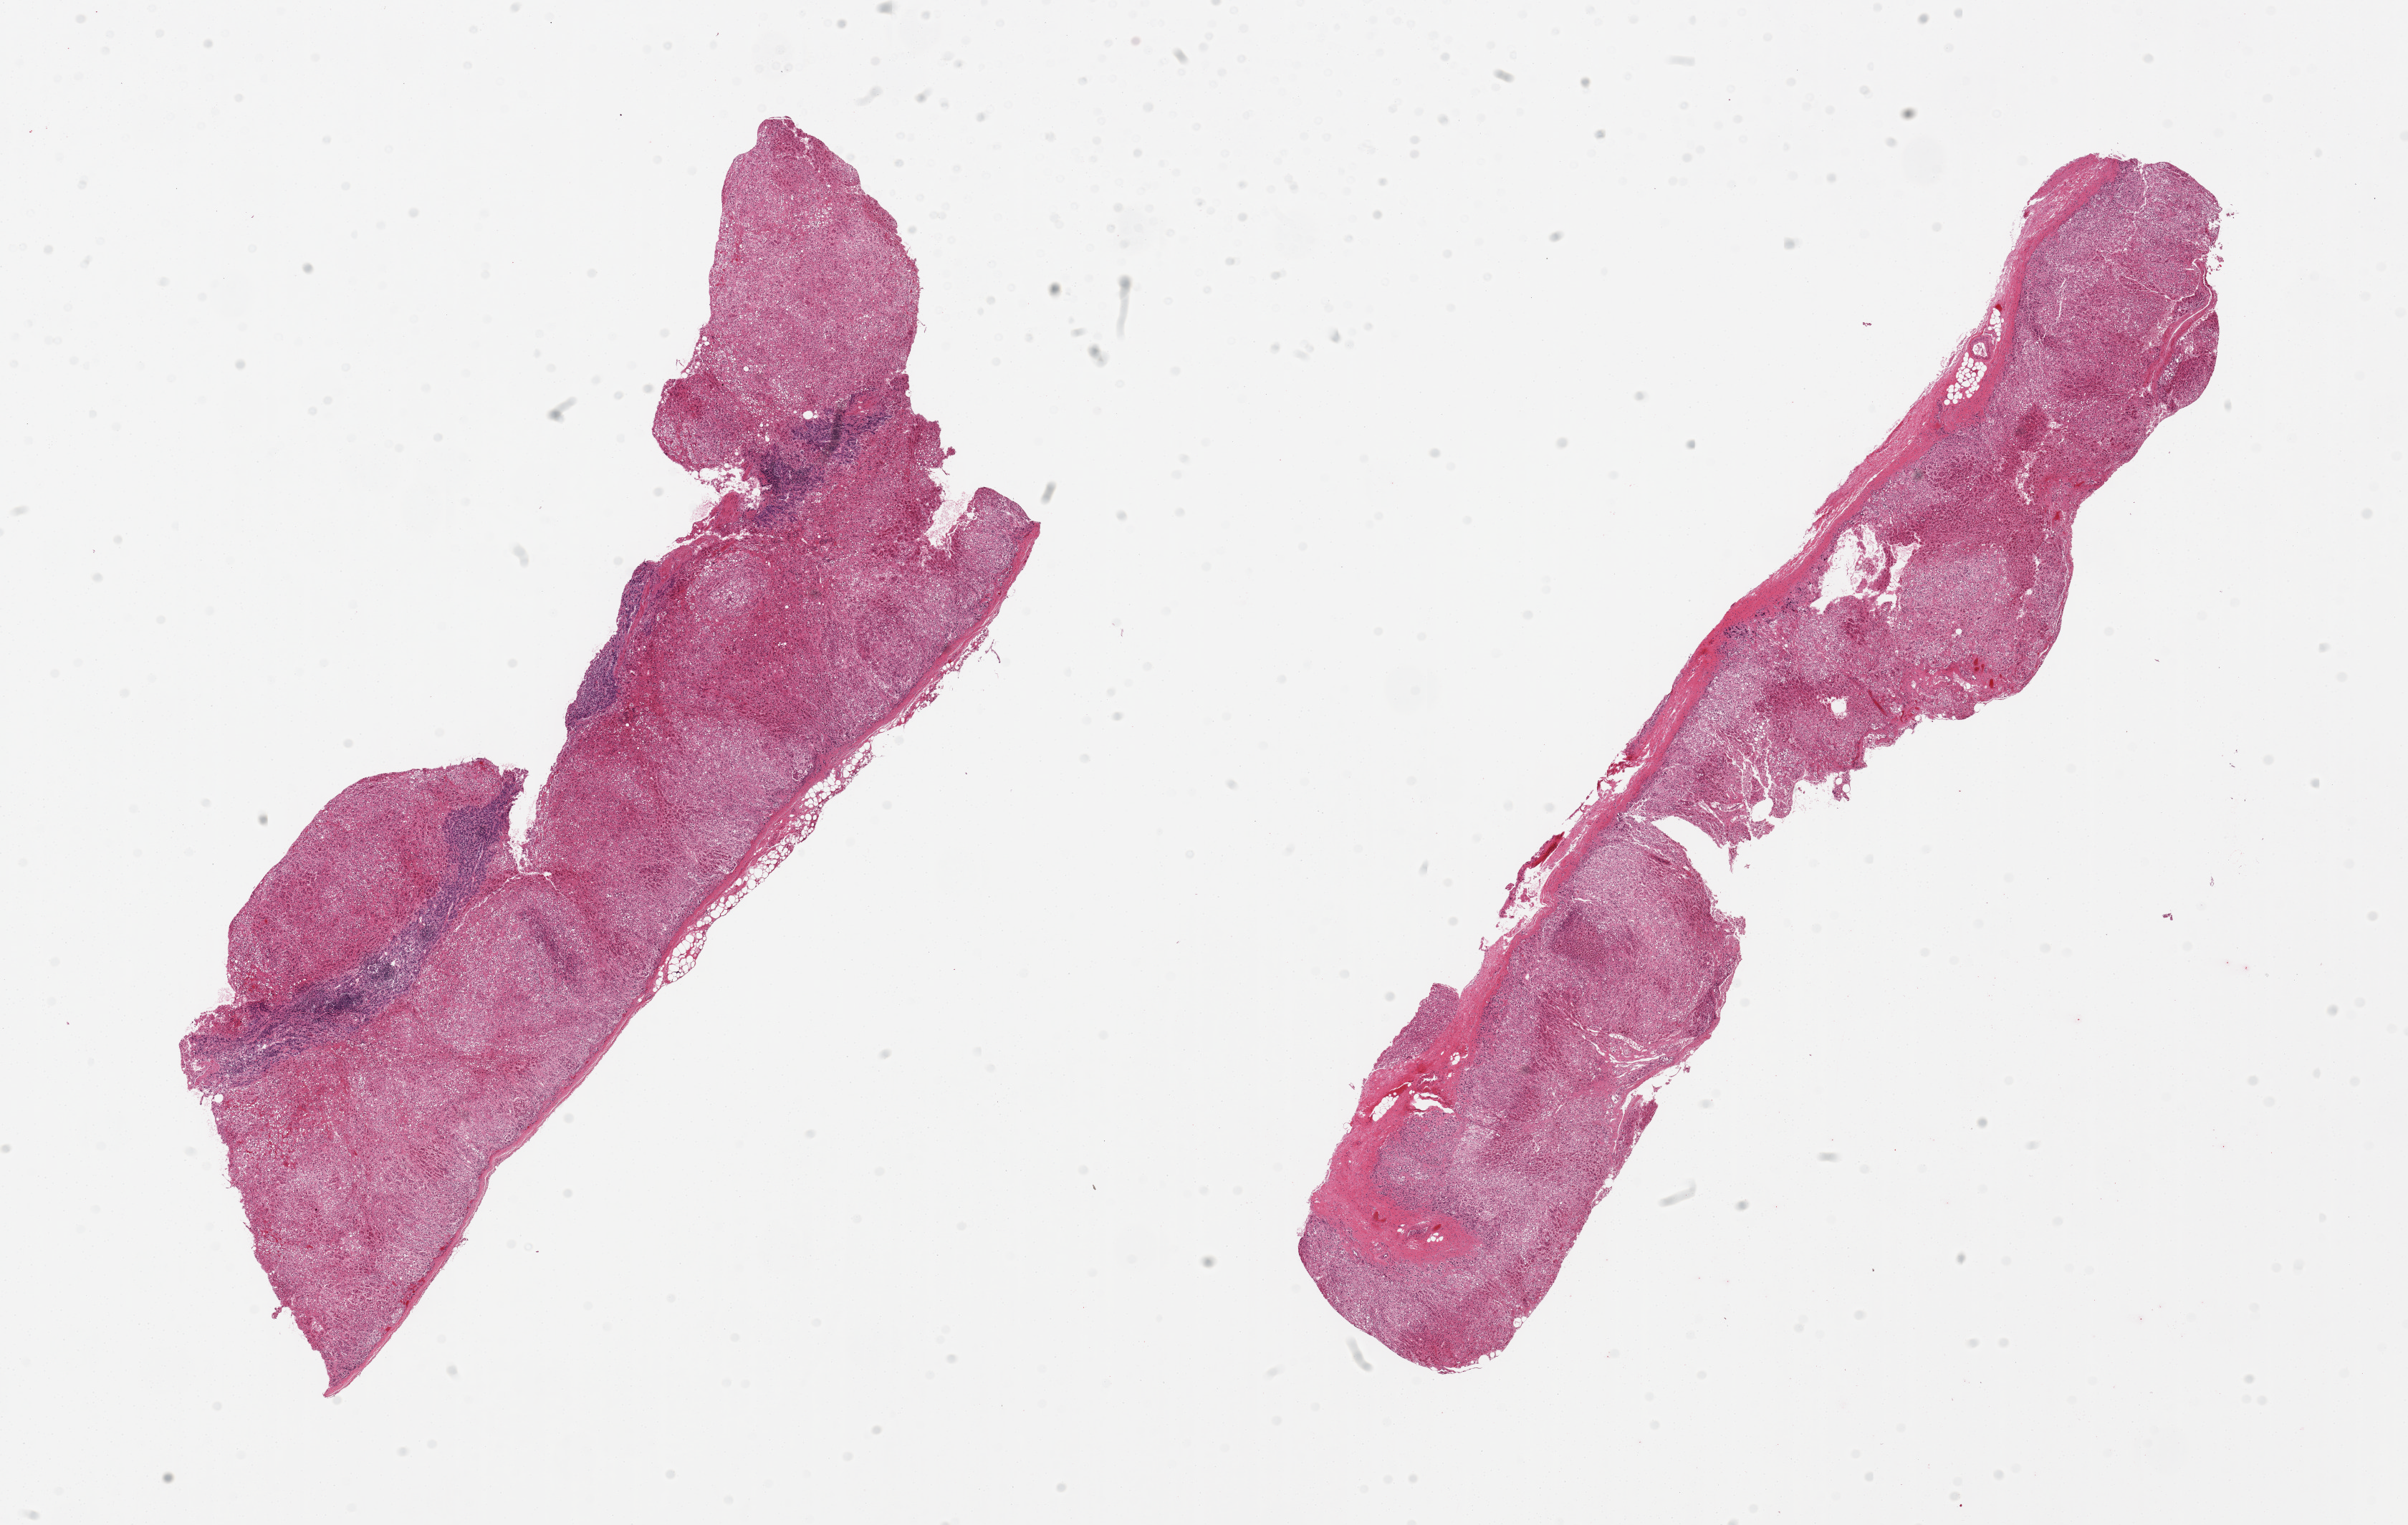
Digitized hematoxylin and eosin (H&E)-stained section, brightfield — shown as a low-resolution overview of the whole scanned area (about 26.6 x 16.8 mm). PAXgene-fixed, paraffin-embedded tissue. Section of adrenal gland (target tissue). Donor tissue sample. Male donor.
Pathologist's review note for this sample: 2 pieces, mainly cortex; foci of medulla visible, but moderately-severely autolyzed.